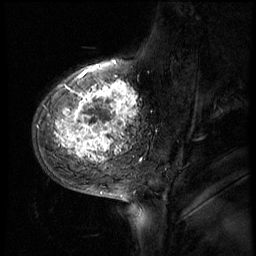
Breast MRI (dynamic contrast-enhanced), one sagittal slice. Position 16 of 56 along the scan axis. 4 images stored at this slice position (order not interpretable as contrast timing). 1.5 T. TE 4.2 ms, TR 8.9 ms. 2.5 mm slice thickness. 256 × 256 image matrix, field of view 220 × 220 mm. Patient: female, 51 years. From the clinical record (not read from this slice): setting: breast cancer imaged before/during neoadjuvant chemotherapy; receptor status: triple-negative.
Structures marked on this image (semi-automatically segmented with operator editing):
- analysis volume of interest (the breast-tissue region the enhancement analysis was run in; not a lesion): box from (x=33, y=70) to (x=150, y=173) px
- tumour enhancement mask (voxels above the 140 % enhancement threshold inside the analysis volume of interest): (x=56, y=72)–(x=138, y=161)